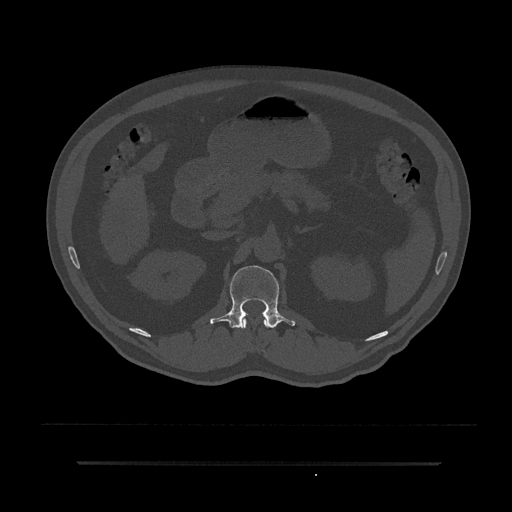
CT including the spine, one axial slice; position 159 of 797 along the scan axis; 120 kVp; bone window (W 1800 / L 400 HU); 512 × 512 image matrix, field of view 464 × 464 mm. Patient: male, 59 years. Case-level facts recorded for this patient, not image findings: primary cancer: bile ducts.
Structures marked on this image (semi-automatically segmented with operator editing):
- L1 vertebra: box from (x=210, y=265) to (x=295, y=328) px
- T12 vertebra: (x=240, y=315)–(x=268, y=329)